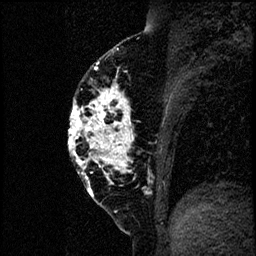
Breast MRI (dynamic contrast-enhanced), one sagittal slice. Position 34 of 60 along the scan axis. Dynamic contrast-enhanced study with each time point stored as its own series, time point 2 of 4 at this slice position (early post-contrast, ordered by acquisition time). 1.5 T. TE 4.2 ms, TR 17.6 ms. 2 mm slice thickness. 256 × 256 image matrix, field of view 200 × 200 mm. Female patient, age 40 years. From the clinical record (not read from this slice): setting: breast cancer imaged before/during neoadjuvant chemotherapy; receptor status: HER2-positive.
Outlined on this slice (semi-automatic segmentation, software-assisted and operator-edited):
- analysis volume of interest (the breast-tissue region the enhancement analysis was run in; not a lesion): box from (x=66, y=55) to (x=185, y=206) px
- tumour enhancement mask (voxels above the 100 % enhancement threshold inside the analysis volume of interest): (x=68, y=62)–(x=130, y=175)